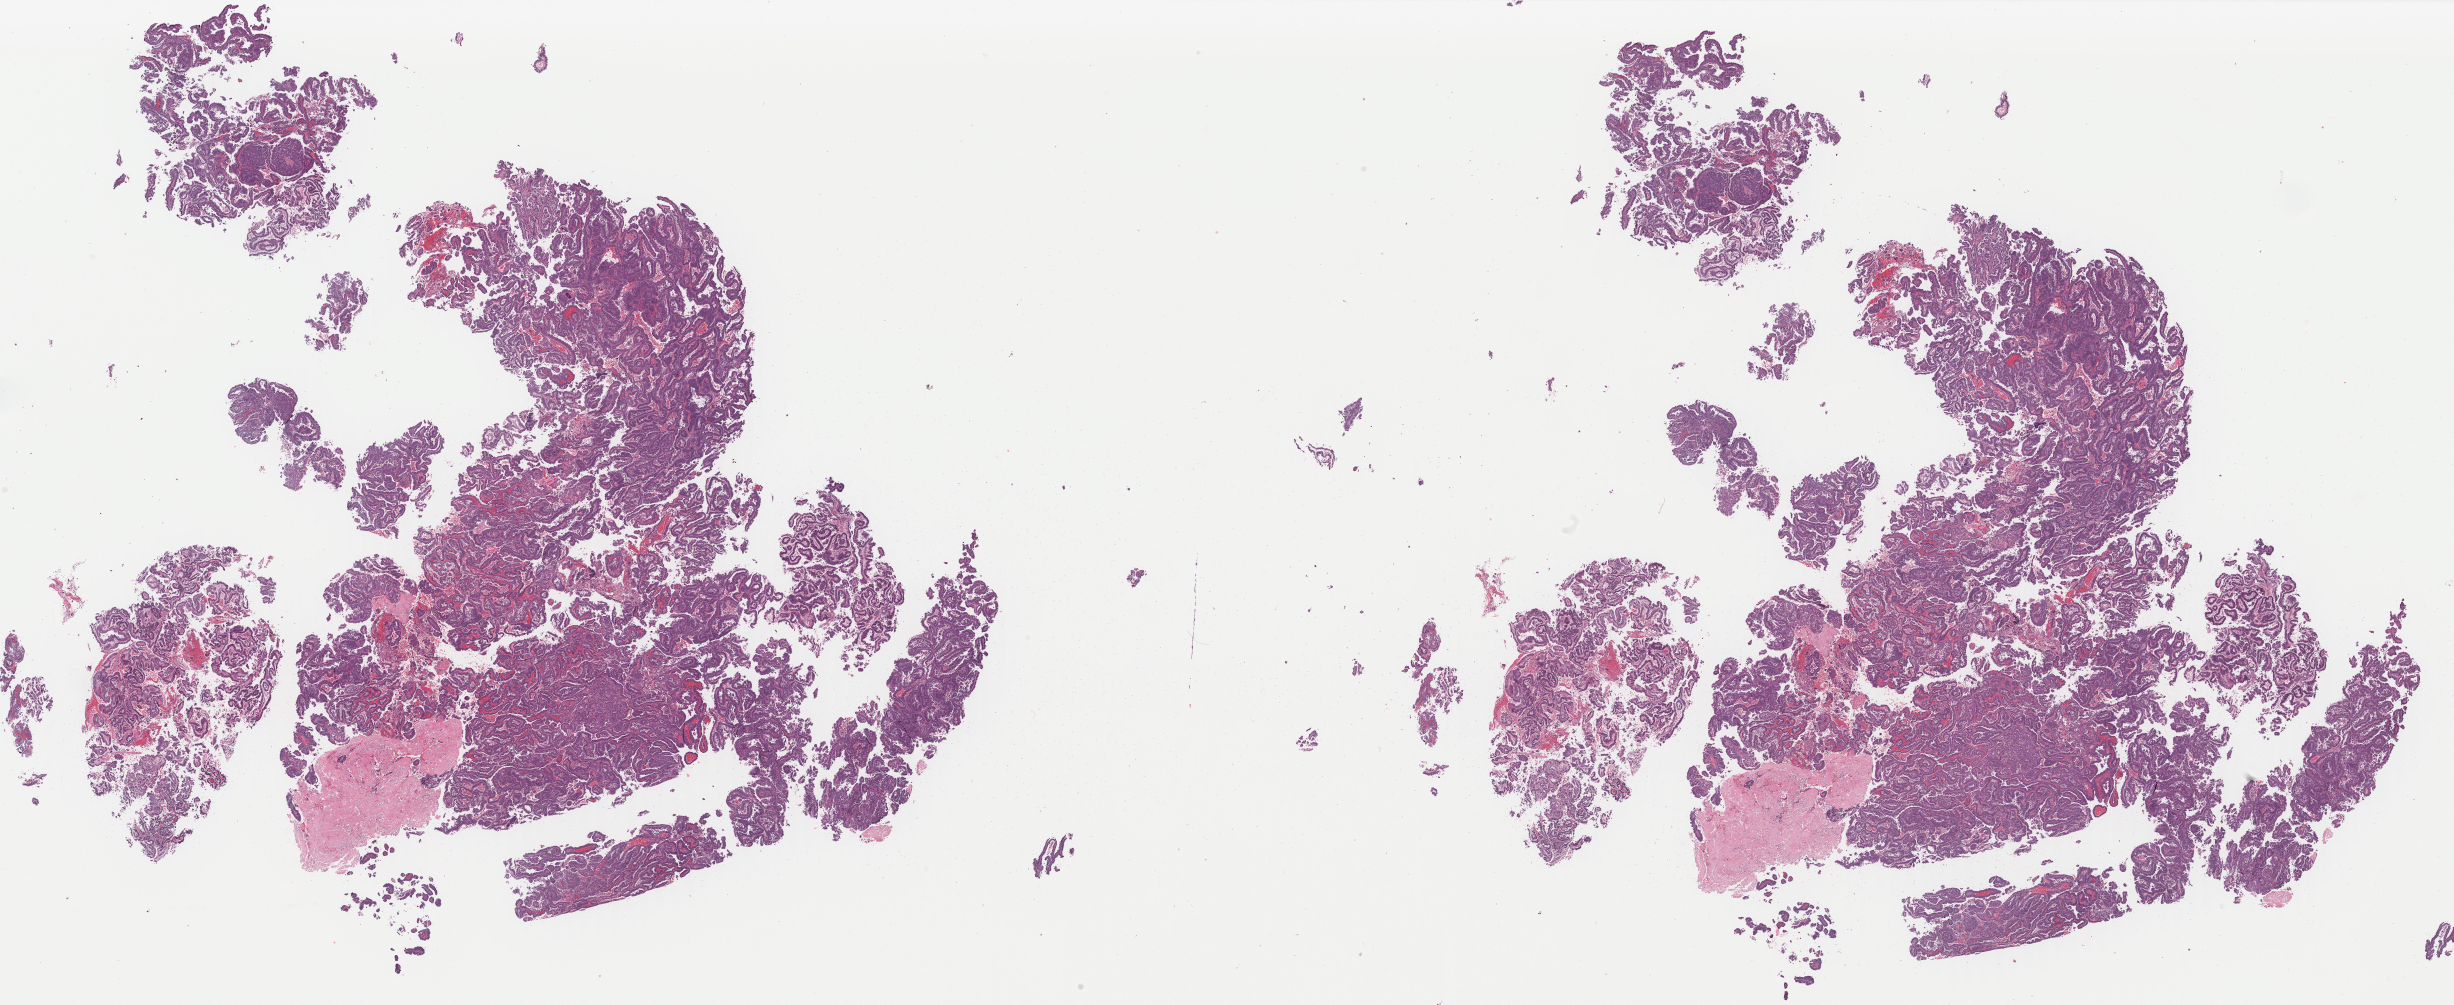
Whole-slide histology image, H&E, a low-resolution overview of the entire scanned area, about 38.8 x 15.9 mm; formalin-fixed paraffin-embedded (FFPE) diagnostic section; uterus, primary tumour sample. Female patient; age at initial diagnosis 83 years. Histologic grade: G3 (poorly differentiated).
Histologic diagnosis: Papillary serous cystadenocarcinoma (endometrium). FIGO stage: IIIC1. Lymph nodes positive (case pathology): 0 of 19 examined.